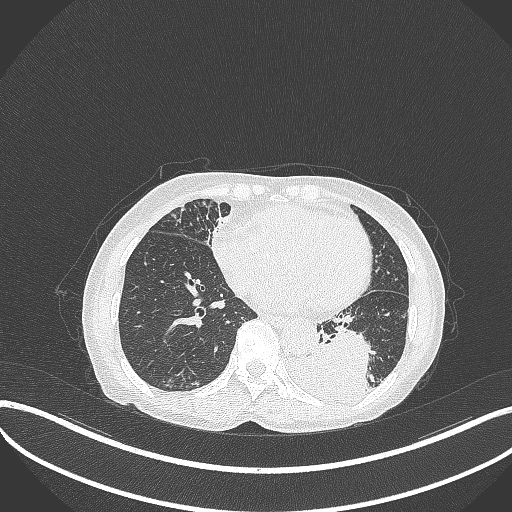
Chest CT, one axial slice; position 106 of 370 along the scan axis; reconstruction kernel B70f; 120 kVp; lung window (W 1500 / L -600 HU); 512 × 512 image matrix, field of view 400 × 400 mm. Female patient, age 78 years. From the clinical record (not read from this slice): clinical TNM (as recorded): T3 N0 M1.
Annotated regions visible in this slice (rectangle marked by the reading radiologist):
- lung tumour (recorded histology: squamous cell carcinoma): box from (x=277, y=328) to (x=374, y=411) px